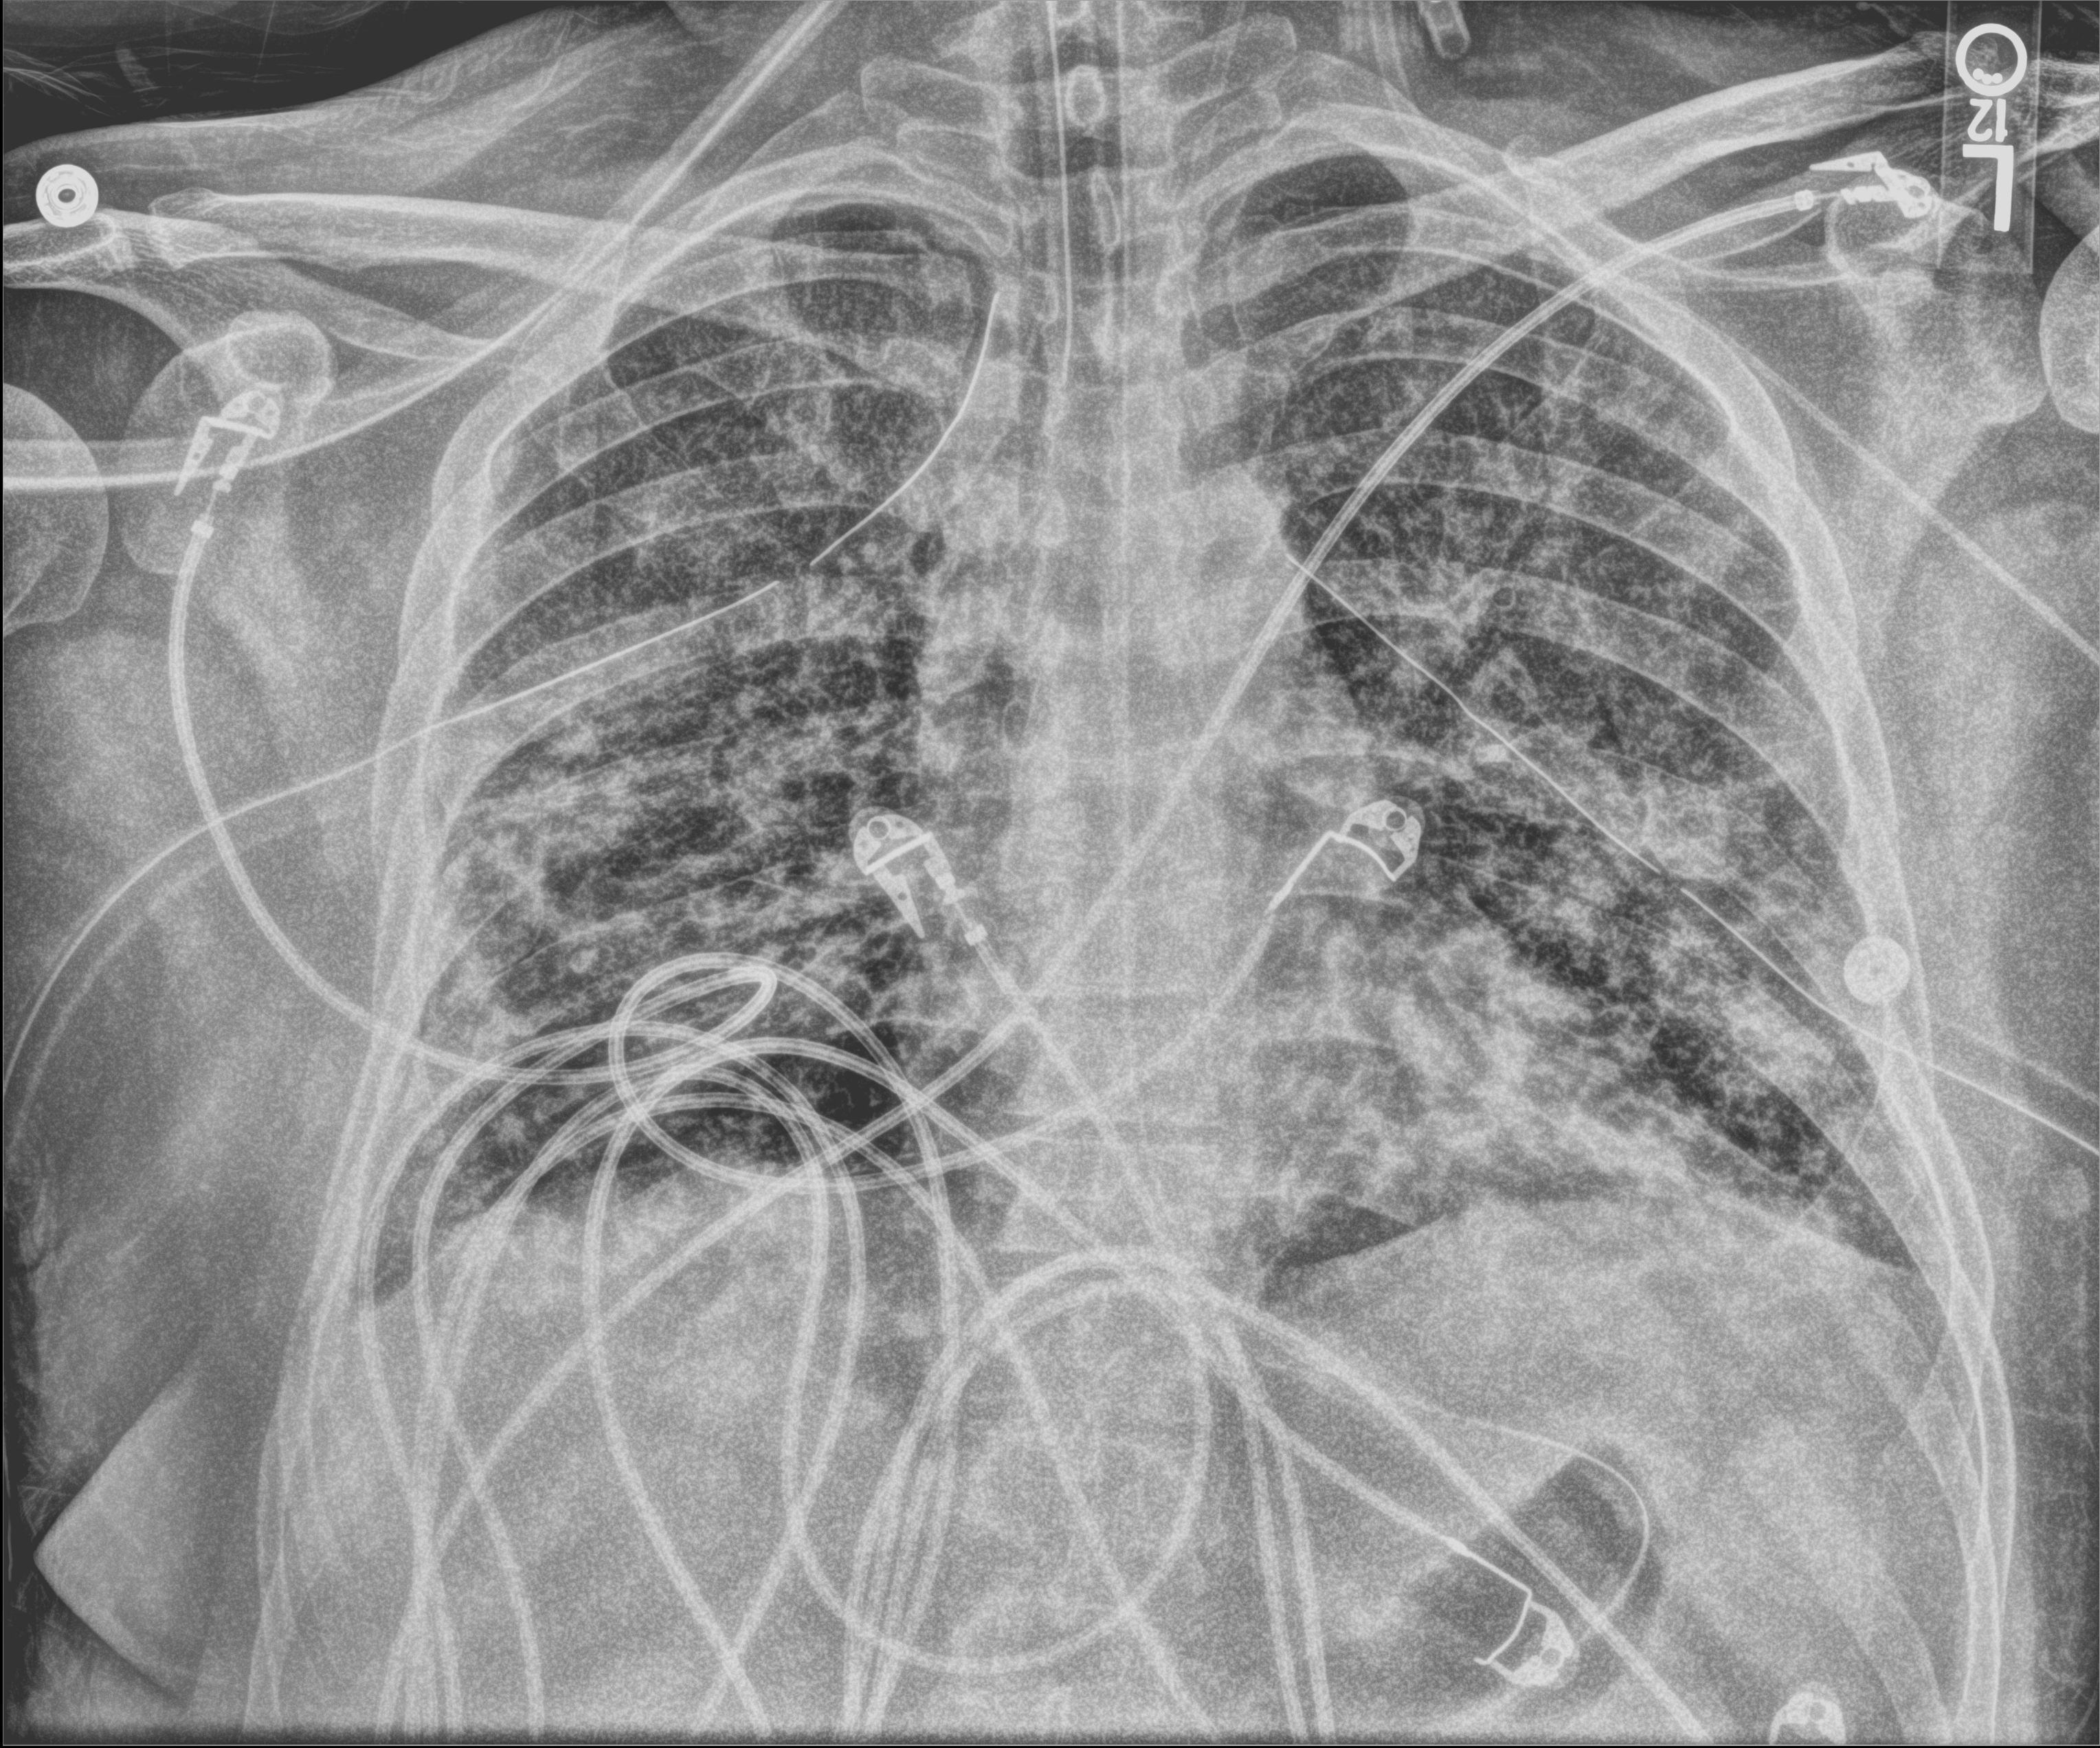
Bedside chest radiograph (computed radiography); anteroposterior (AP) projection. Male patient hospitalised with COVID-19, age 18–59 years.
Hospital-stay facts (about this admission, not read from this image; timing relative to this image not recorded):
- mechanically ventilated during this hospital stay: yes